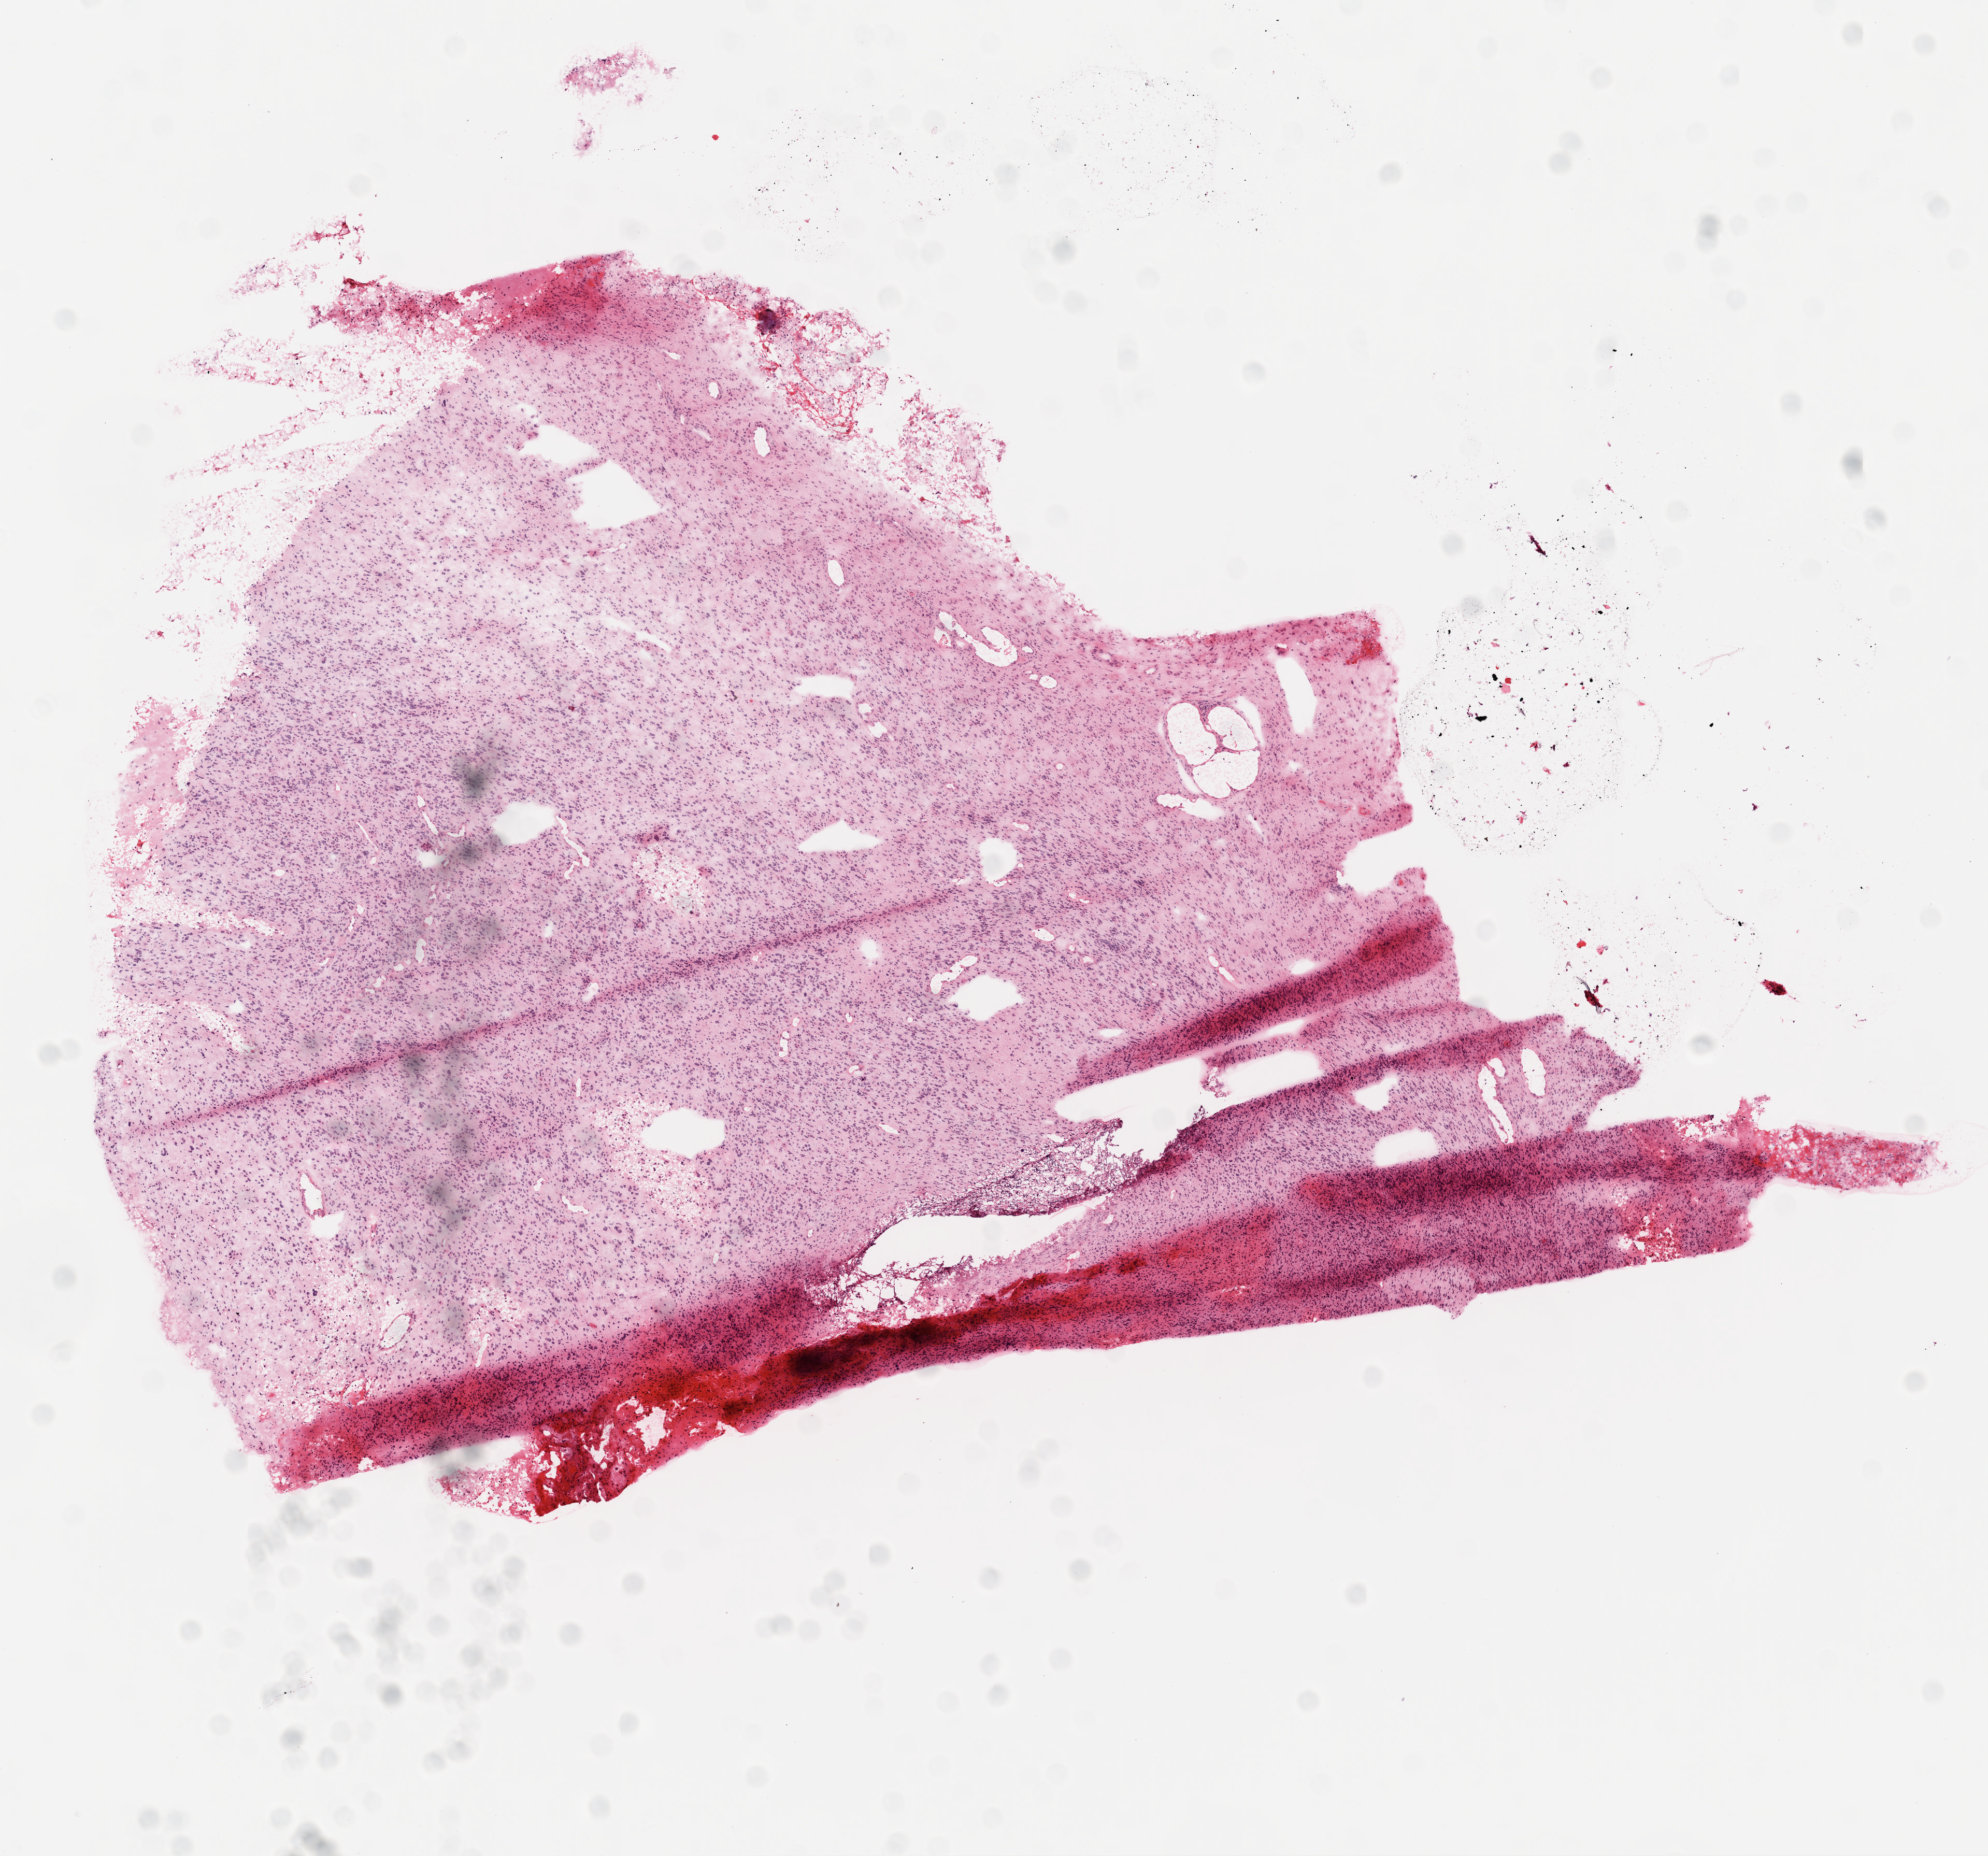
Digitized H&E tissue section (whole slide), low-resolution overview of the scanned area, about 7.7 x 7.2 mm (from a 20x scan). Frozen section from the top of the tissue portion. Brain, primary tumour sample. Patient: female, age at initial diagnosis 59 years. Composition of this section per pathologist review: tumour cells 70%, tumour nuclei 90%, normal cells 0%, stromal cells 25%, necrosis 5%.
Pathologic diagnosis: Glioblastoma.